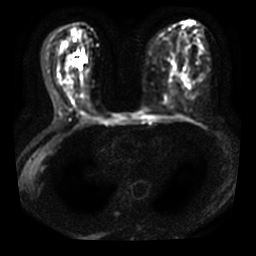
Breast MRI, one axial slice. Slice 17 of 40 in the series (ordered by position). Diffusion-weighted series; image 2 of 4 stored at this slice position (different b-values; order by instance number). 3 T. 256 × 256 image matrix, field of view 320 × 320 mm. Female patient.
Outlined on this slice (manually delineated by an expert):
- tumour on diffusion-weighted imaging: bounding box (x1, y1, x2, y2) in pixels: (75, 59, 82, 67)